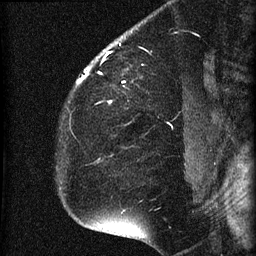
Breast MRI (dynamic contrast-enhanced), one sagittal slice; position 50 of 60 along the scan axis; dynamic contrast-enhanced series, image 2 of 4 at this slice position (ordered by acquisition); 1.5 T; TE 4.2 ms, TR 22.7 ms; 1.5 mm slice thickness; 256 × 256 image matrix. Patient: female, 35 years. From the clinical record (not read from this slice): setting: breast cancer imaged before/during neoadjuvant chemotherapy; receptor status: HR-positive, HER2-negative.
Annotated regions visible in this slice (semi-automatic segmentation, software-assisted and operator-edited):
- analysis volume of interest (the breast-tissue region the enhancement analysis was run in; not a lesion): bounding box (x1, y1, x2, y2) in pixels: (69, 27, 199, 112)
- tumour enhancement mask (voxels above the 90 % enhancement threshold inside the analysis volume of interest): (77, 52, 112, 103)